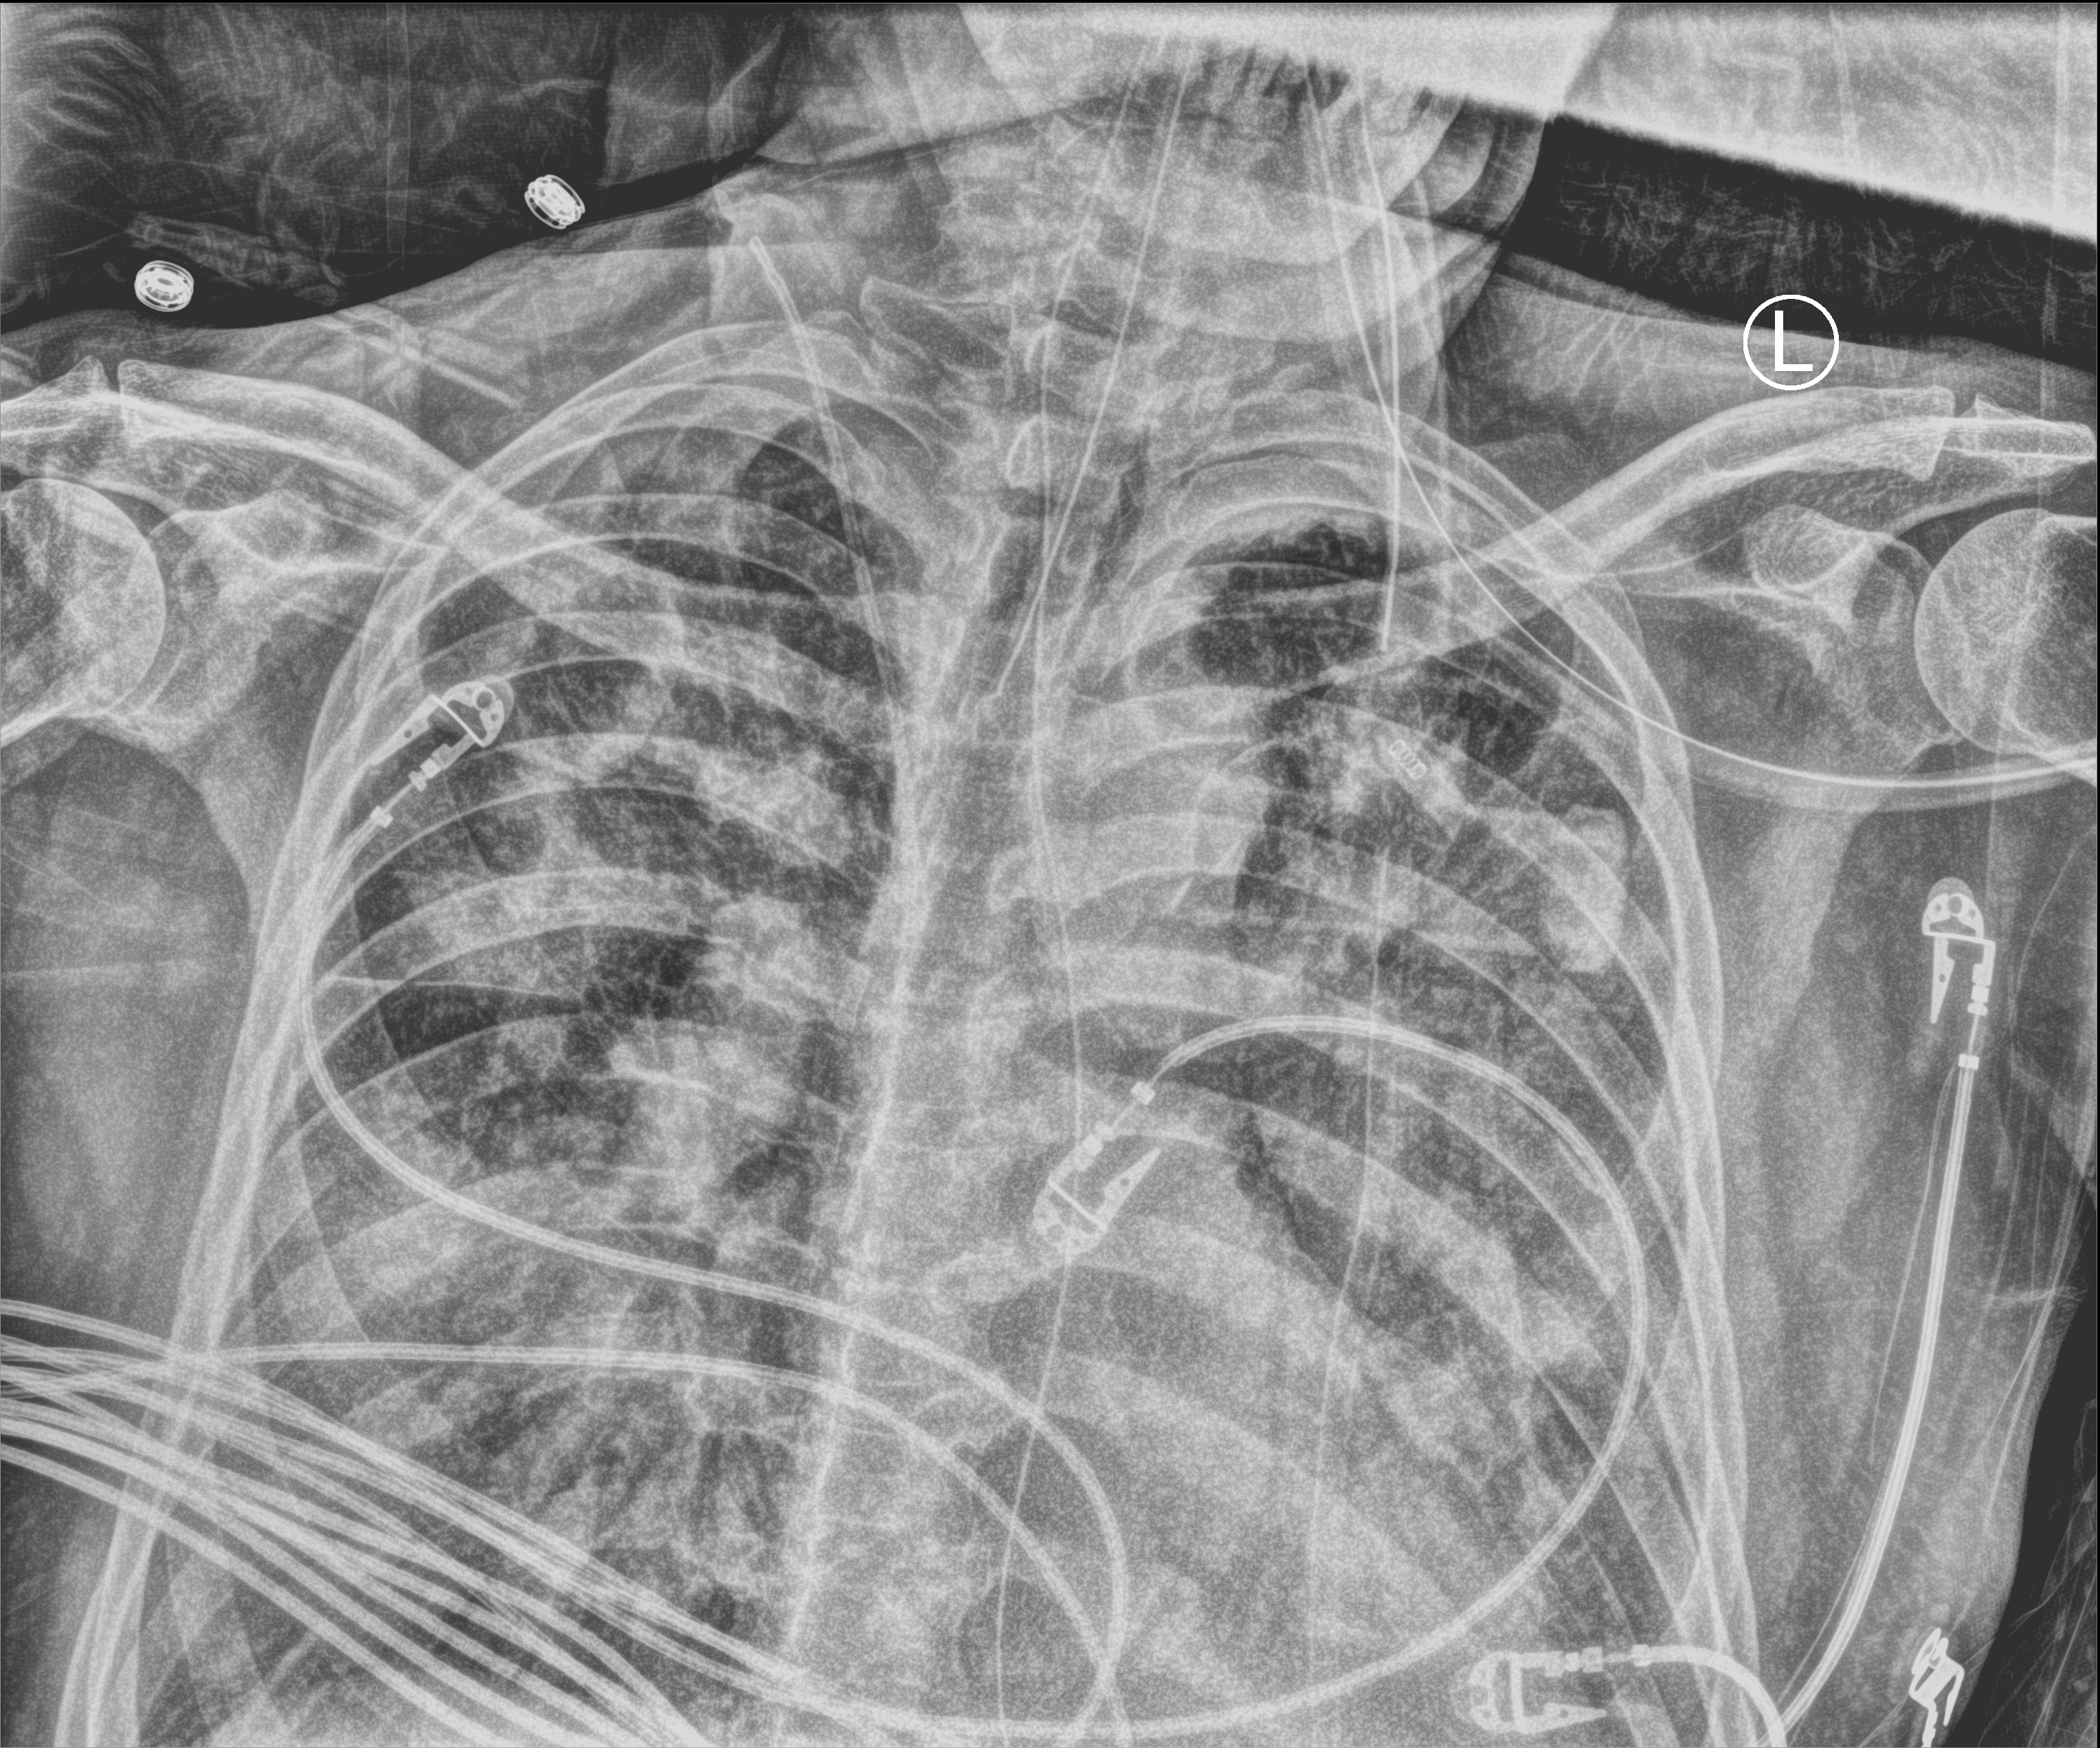
Portable chest radiograph; anteroposterior (AP) projection. Male patient hospitalised with COVID-19, age 60–74 years.
Admission-level facts for this patient (not findings on this image; timing relative to this image not recorded):
- hypertension (admission record): no
- COPD (admission record): no
- mechanically ventilated during this hospital stay: yes